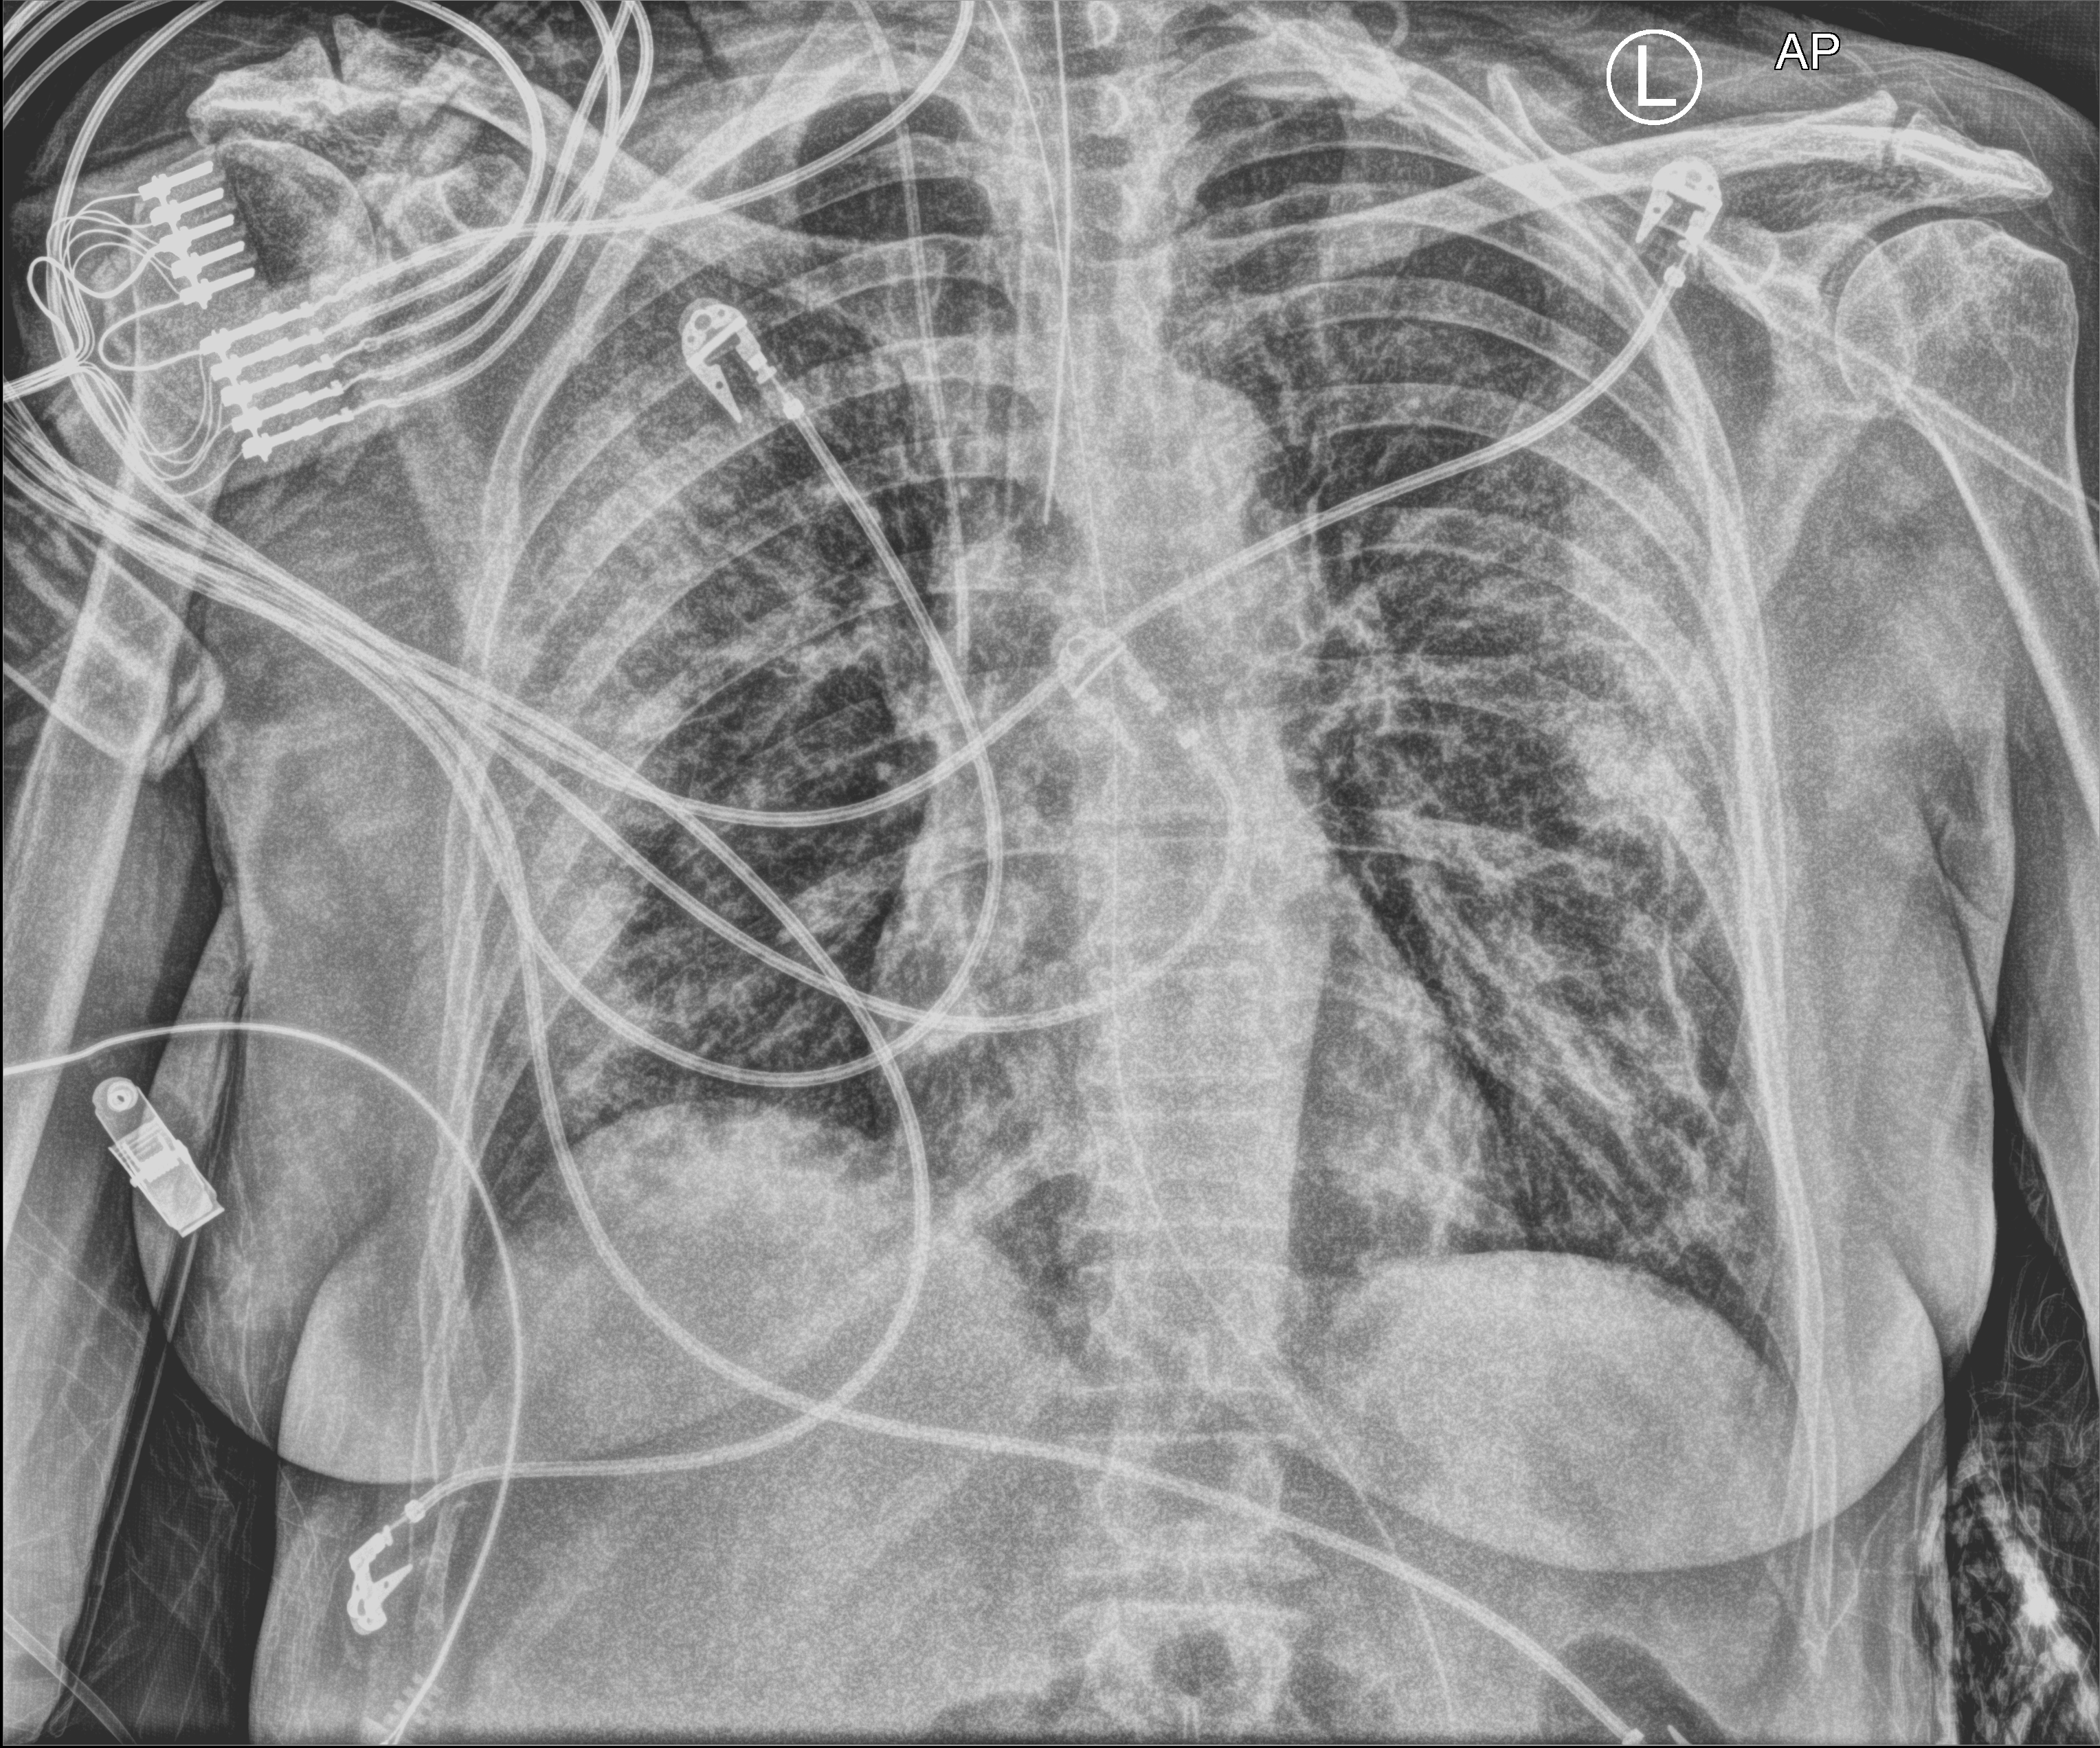
Chest X-ray (portable), anteroposterior (AP) projection. Patient hospitalised with COVID-19; female, aged 60–74 years.
Admission-level facts for this patient (not findings on this image; timing relative to this image not recorded): length of hospital stay: 18 days.